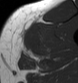
MRI of an extremity soft-tissue mass, one axial slice. Position 31 of 43 along the scan axis. MR volume resampled by the dataset authors to the PET/CT grid (not the native acquisition matrix). 3.27 mm slice thickness. 78 × 83 image matrix. Male patient. Case-level facts recorded for this patient, not image findings: histological type: pleiomorphic leiomyosarcoma; grade: high; site of the primary tumour: left thigh.
Annotated regions visible in this slice (expert contour drawn on MRI and transferred to this co-registered scan by the dataset authors):
- gross tumour volume including surrounding oedema: bounding box [x1, y1, x2, y2] px = [20, 26, 44, 59]
- gross tumour volume (mass): [27, 44, 37, 55]